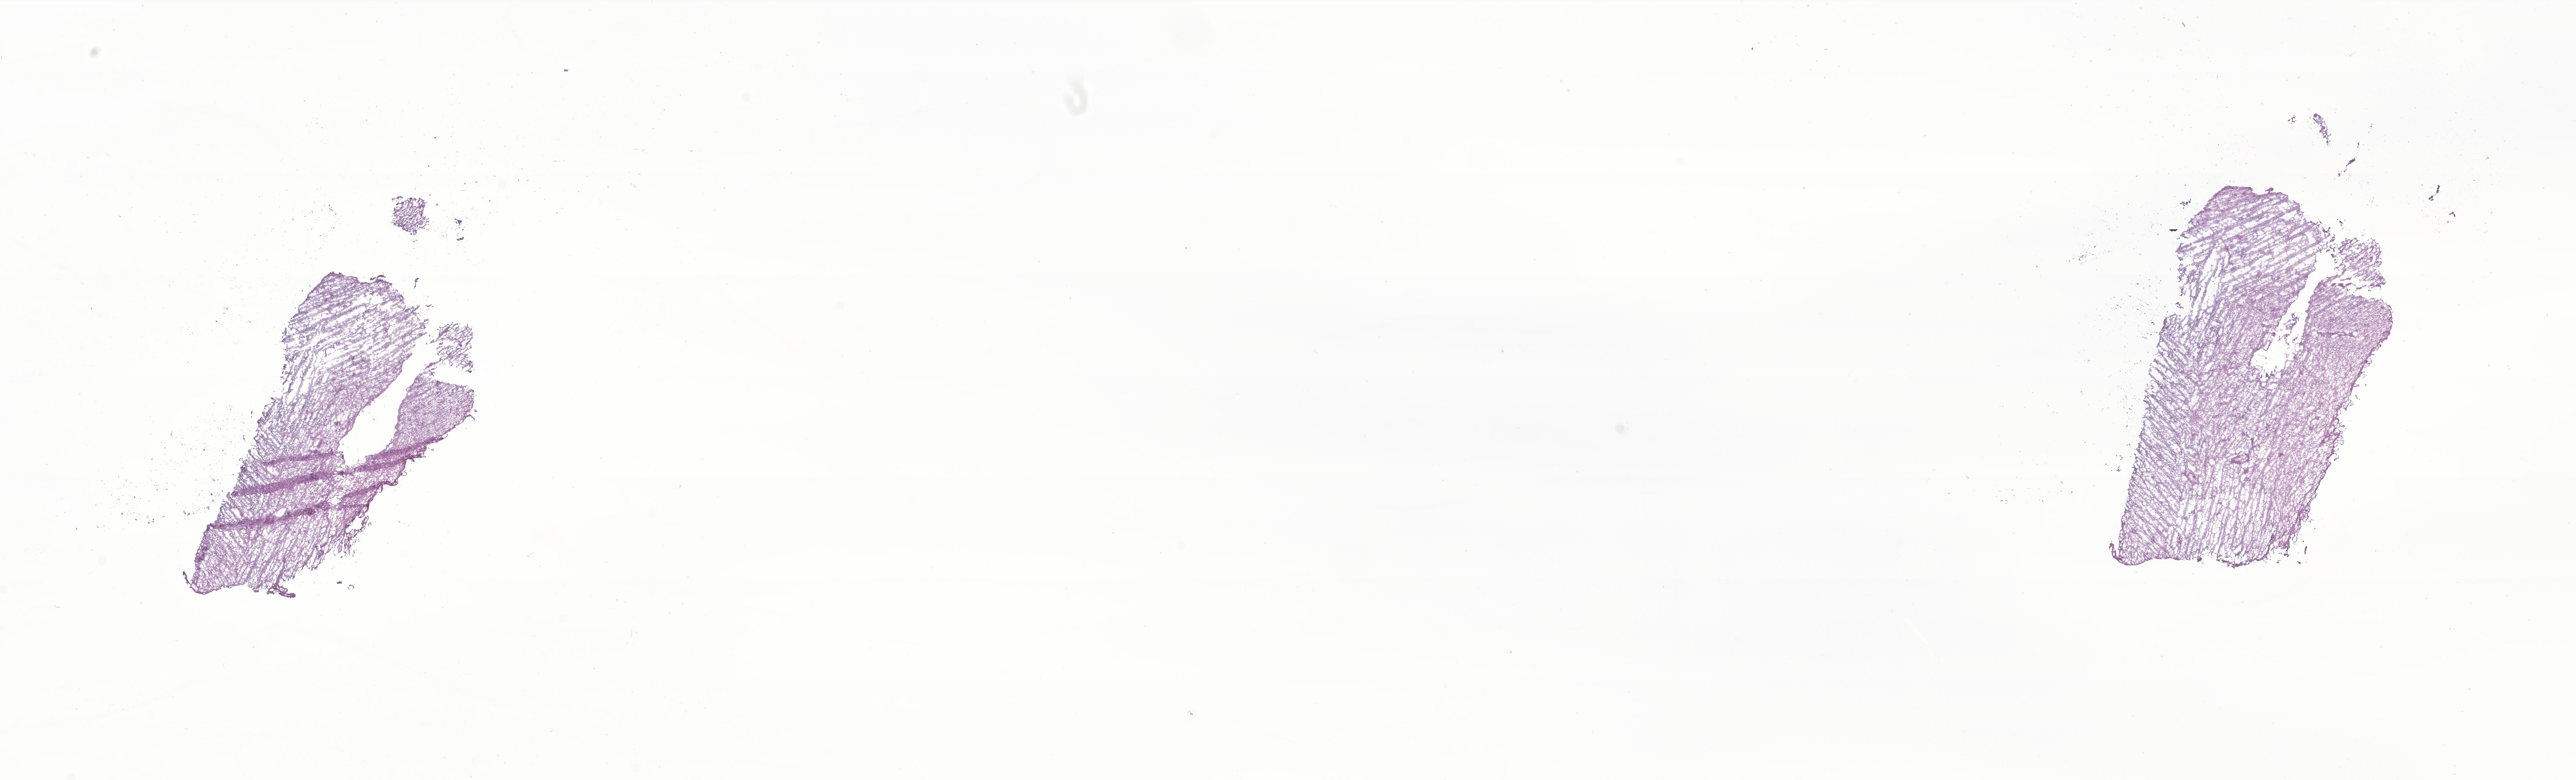
Whole-slide image, haematoxylin and eosin stain of tumor tissue from the brain, a low-resolution overview of the entire scanned area, about 27.1 x 8.2 mm. Frozen section (OCT-embedded). Patient: male, age 915 days (about 2.5 years).
Diagnosis: Neoplasm, malignant.